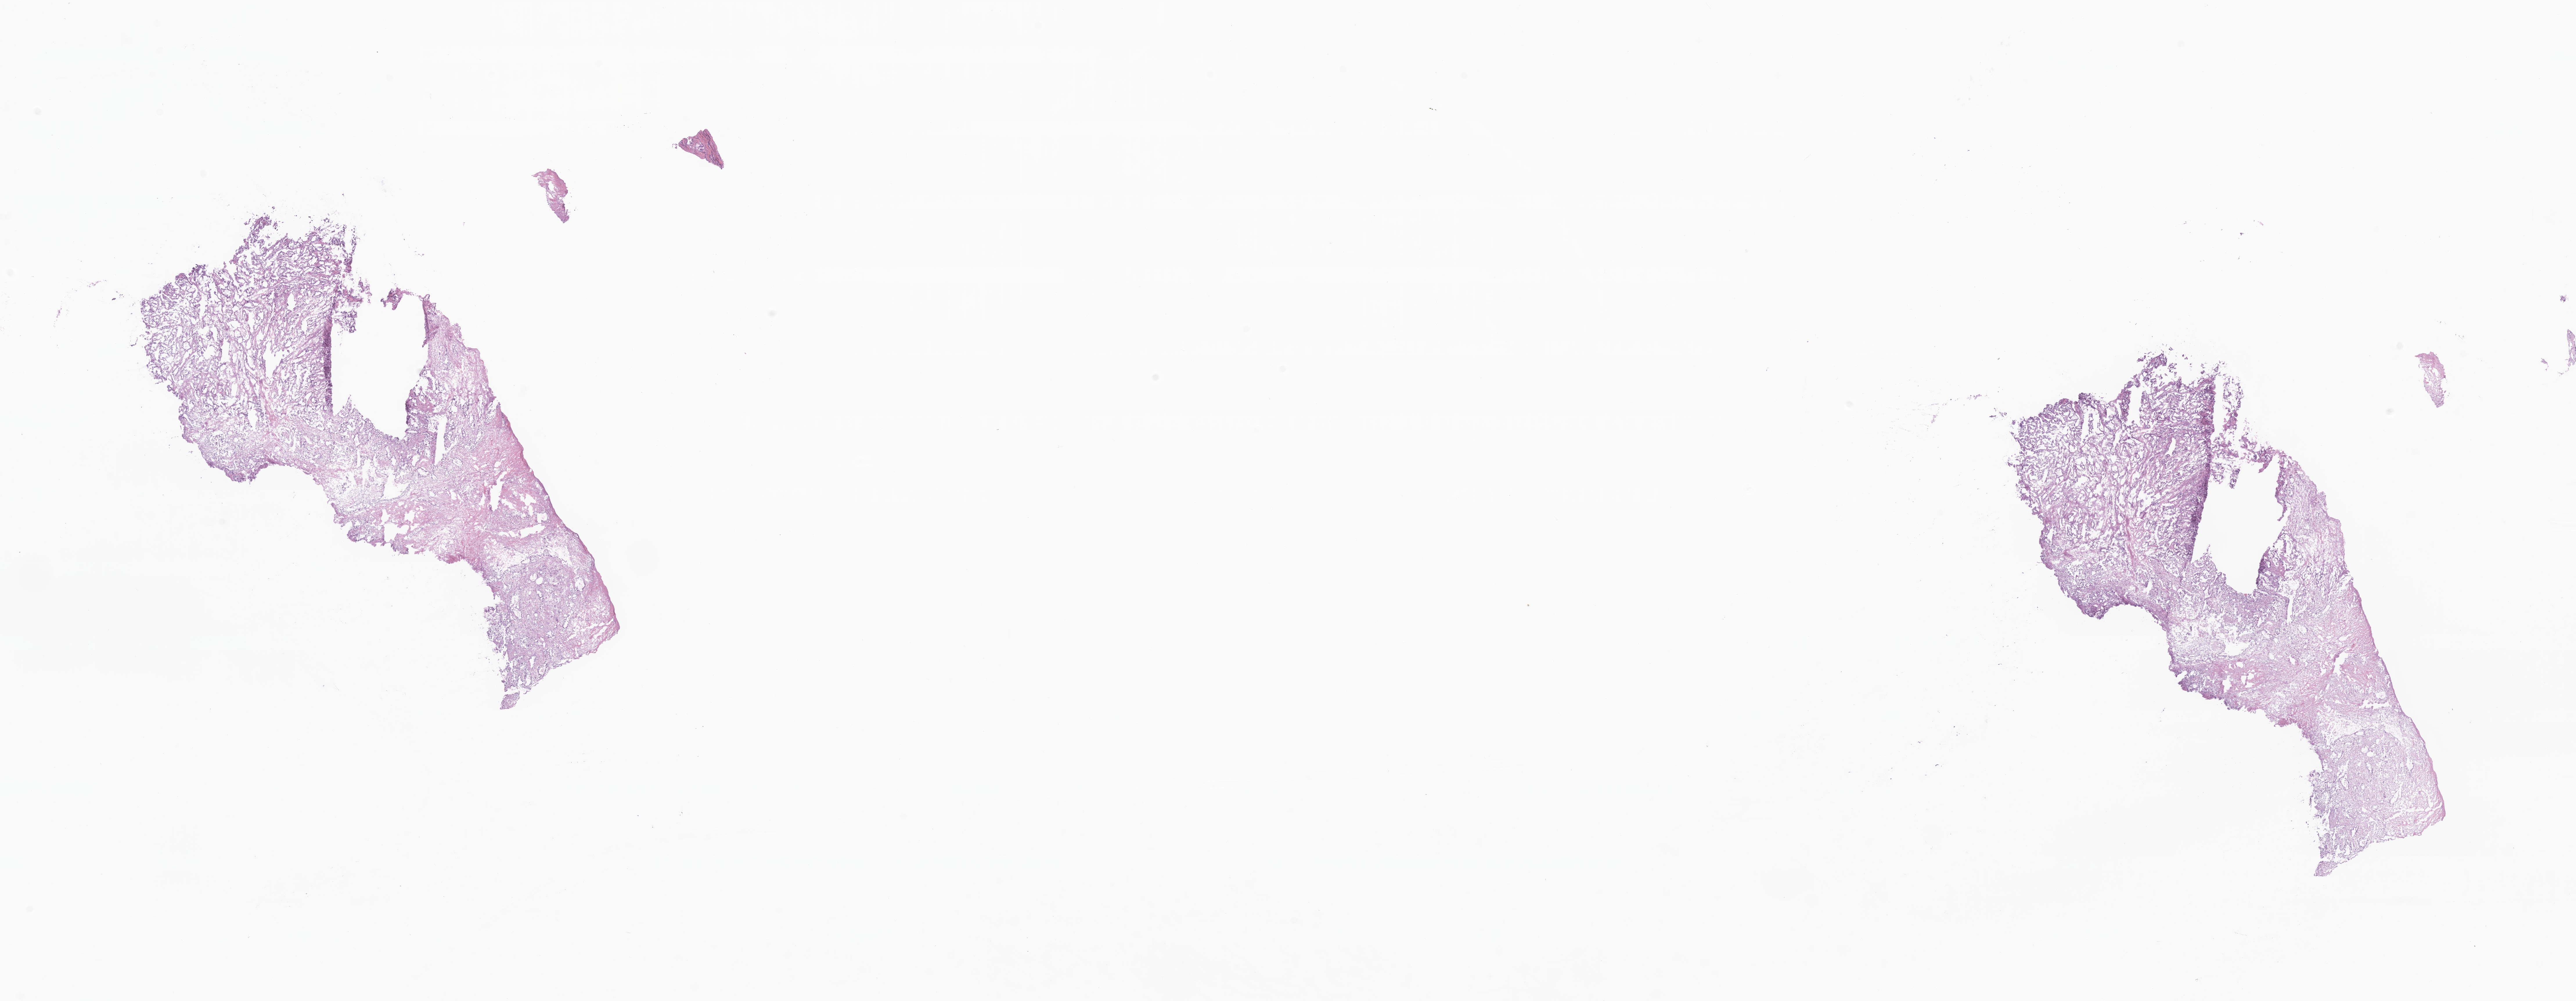
H&E whole-slide image — a low-resolution overview of the entire scanned area, about 37.4 x 14.5 mm, frozen section, specimen: primary tumor, site: head of pancreas. Male patient; age at initial diagnosis 77 years. Tumor grade: G2 (moderately differentiated). Pathologist review of this section (percent, as recorded): tumor cells 80%, tumor nuclei 80%, stromal cells 18%, necrosis 0%, normal cells 2%. Inflammatory infiltration, as recorded: lymphocyte infiltration 5%, monocyte infiltration 2%, neutrophil infiltration 6%.
* histologic diagnosis: Intraductal papillary mucinous neoplasm with invasive carcinoma
* AJCC pathologic stage: Stage IB
* section: top of the tissue portion